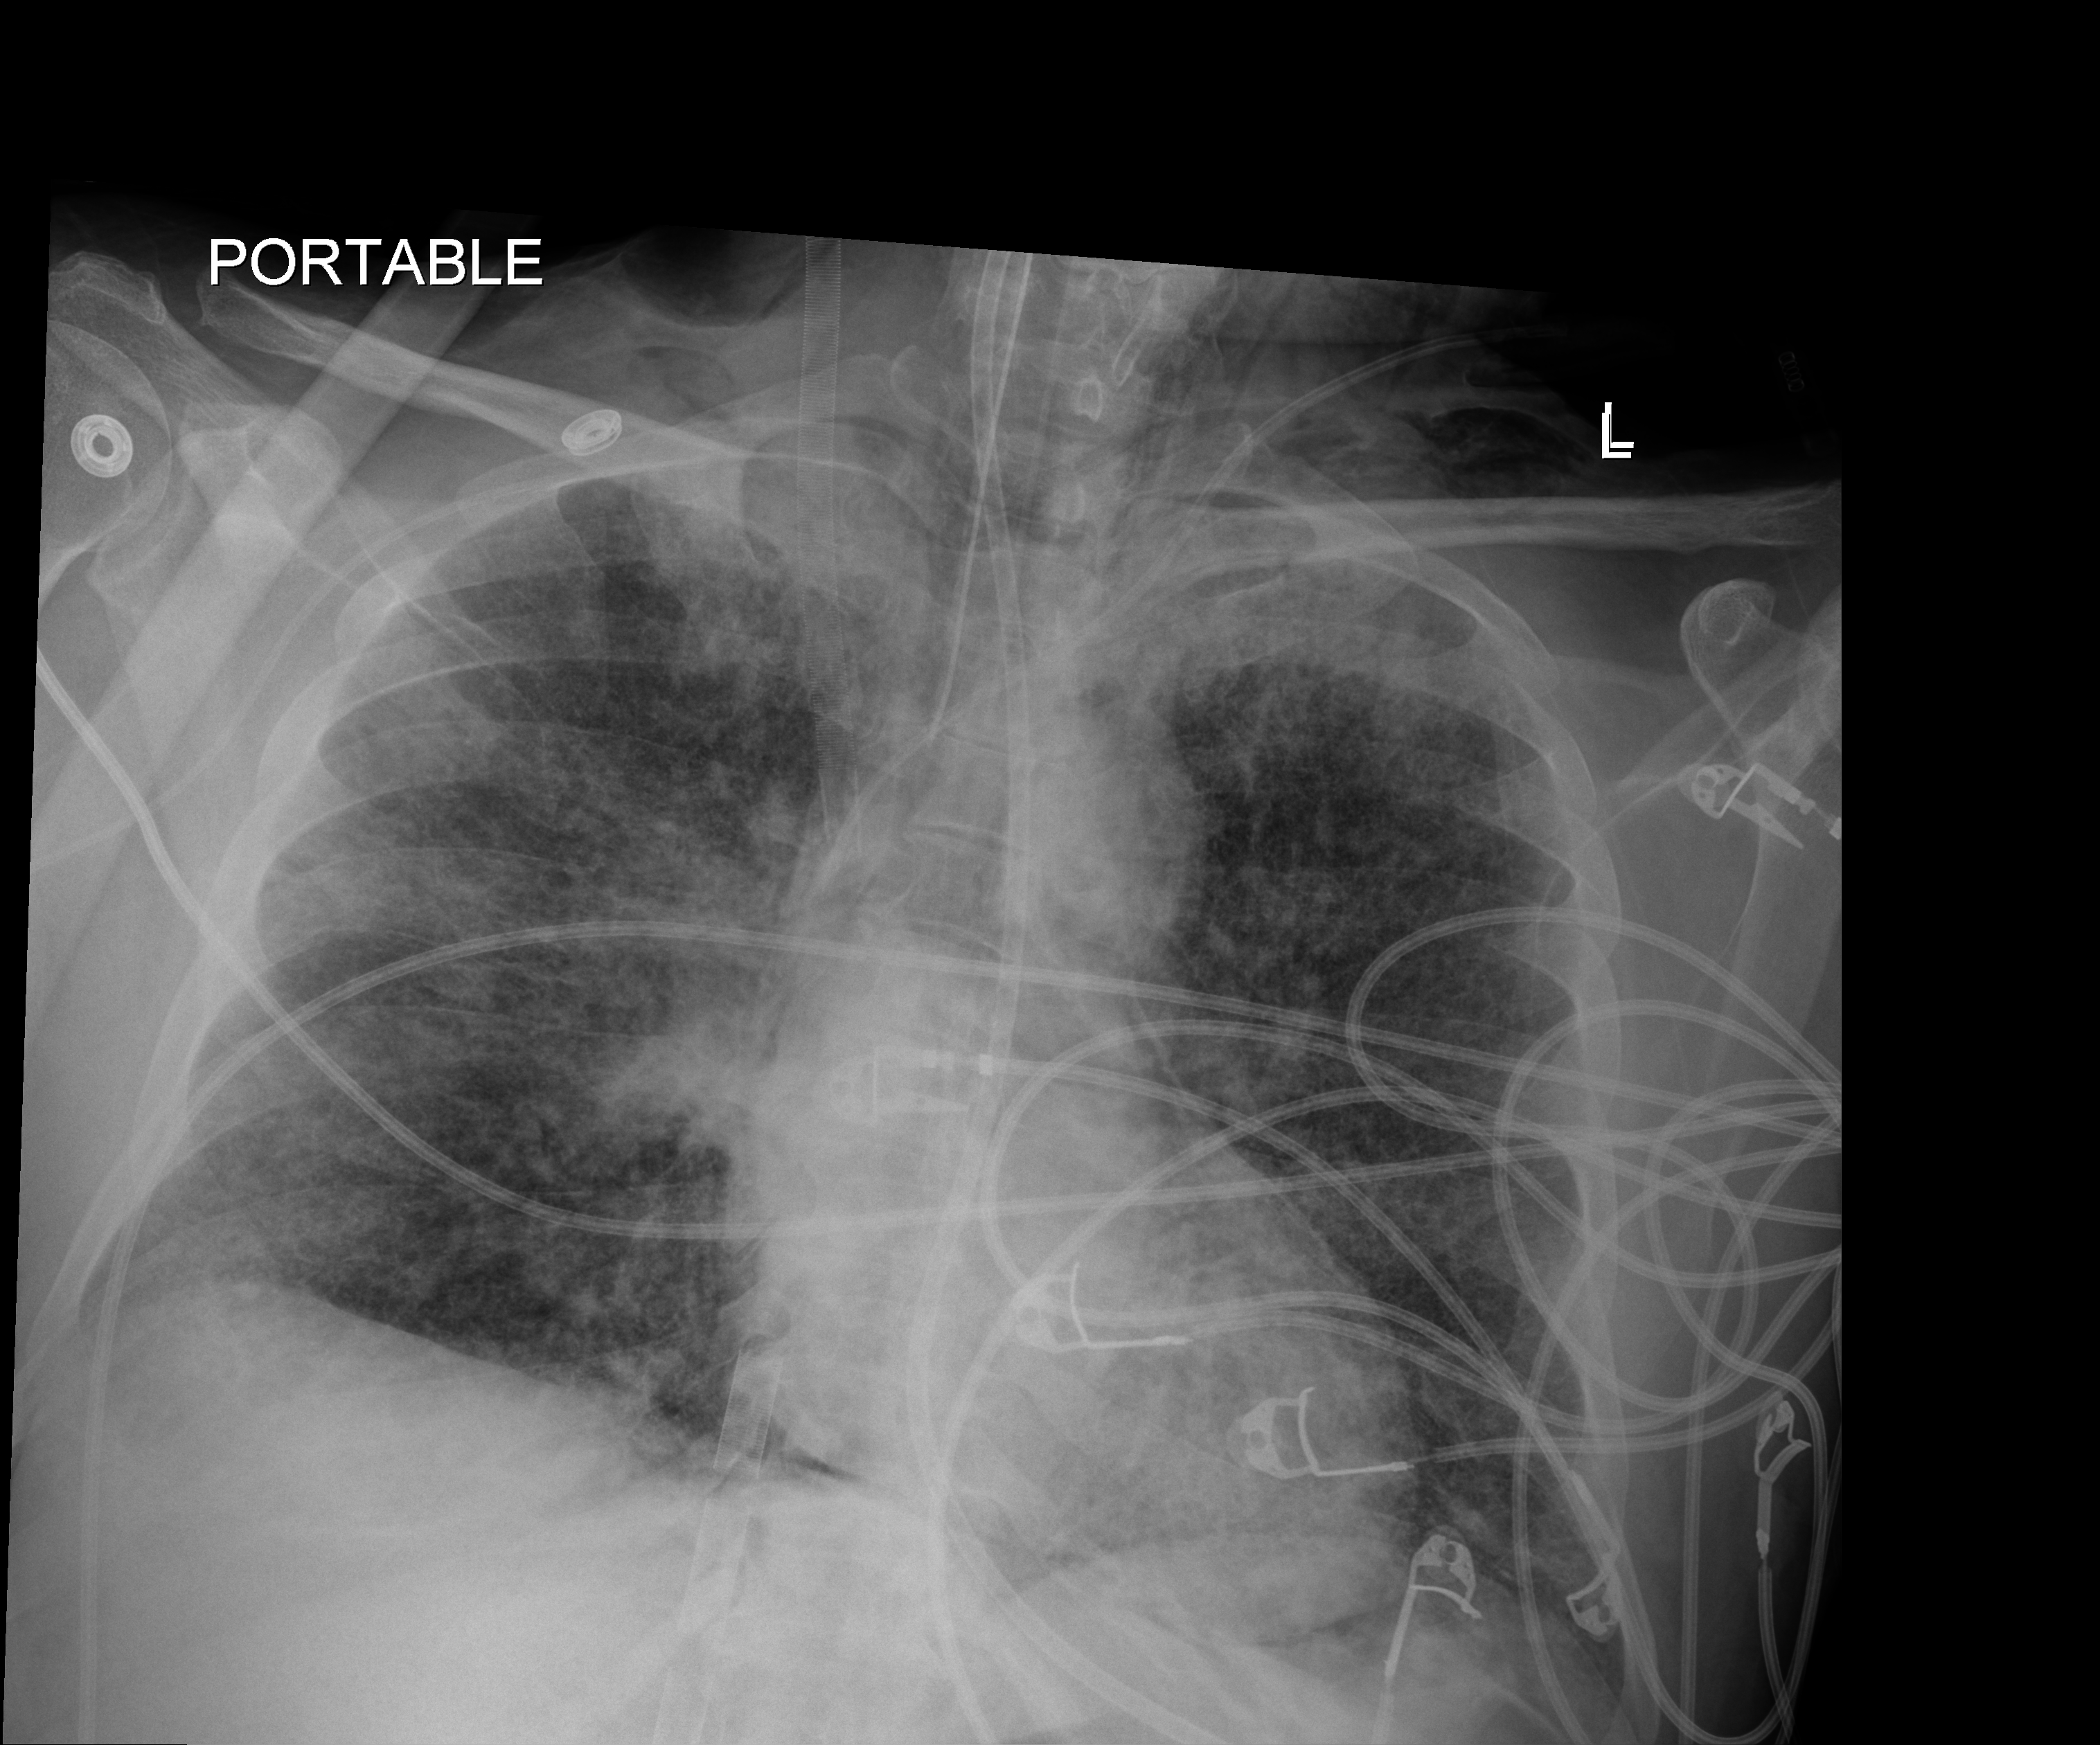
Chest X-ray, anteroposterior (AP) projection. Male patient hospitalised with COVID-19, age 18–59 years.
Hospital-stay facts (about this admission, not read from this image; timing relative to this image not recorded): admitted to intensive care during this hospital stay: yes; mechanically ventilated during this hospital stay: yes.